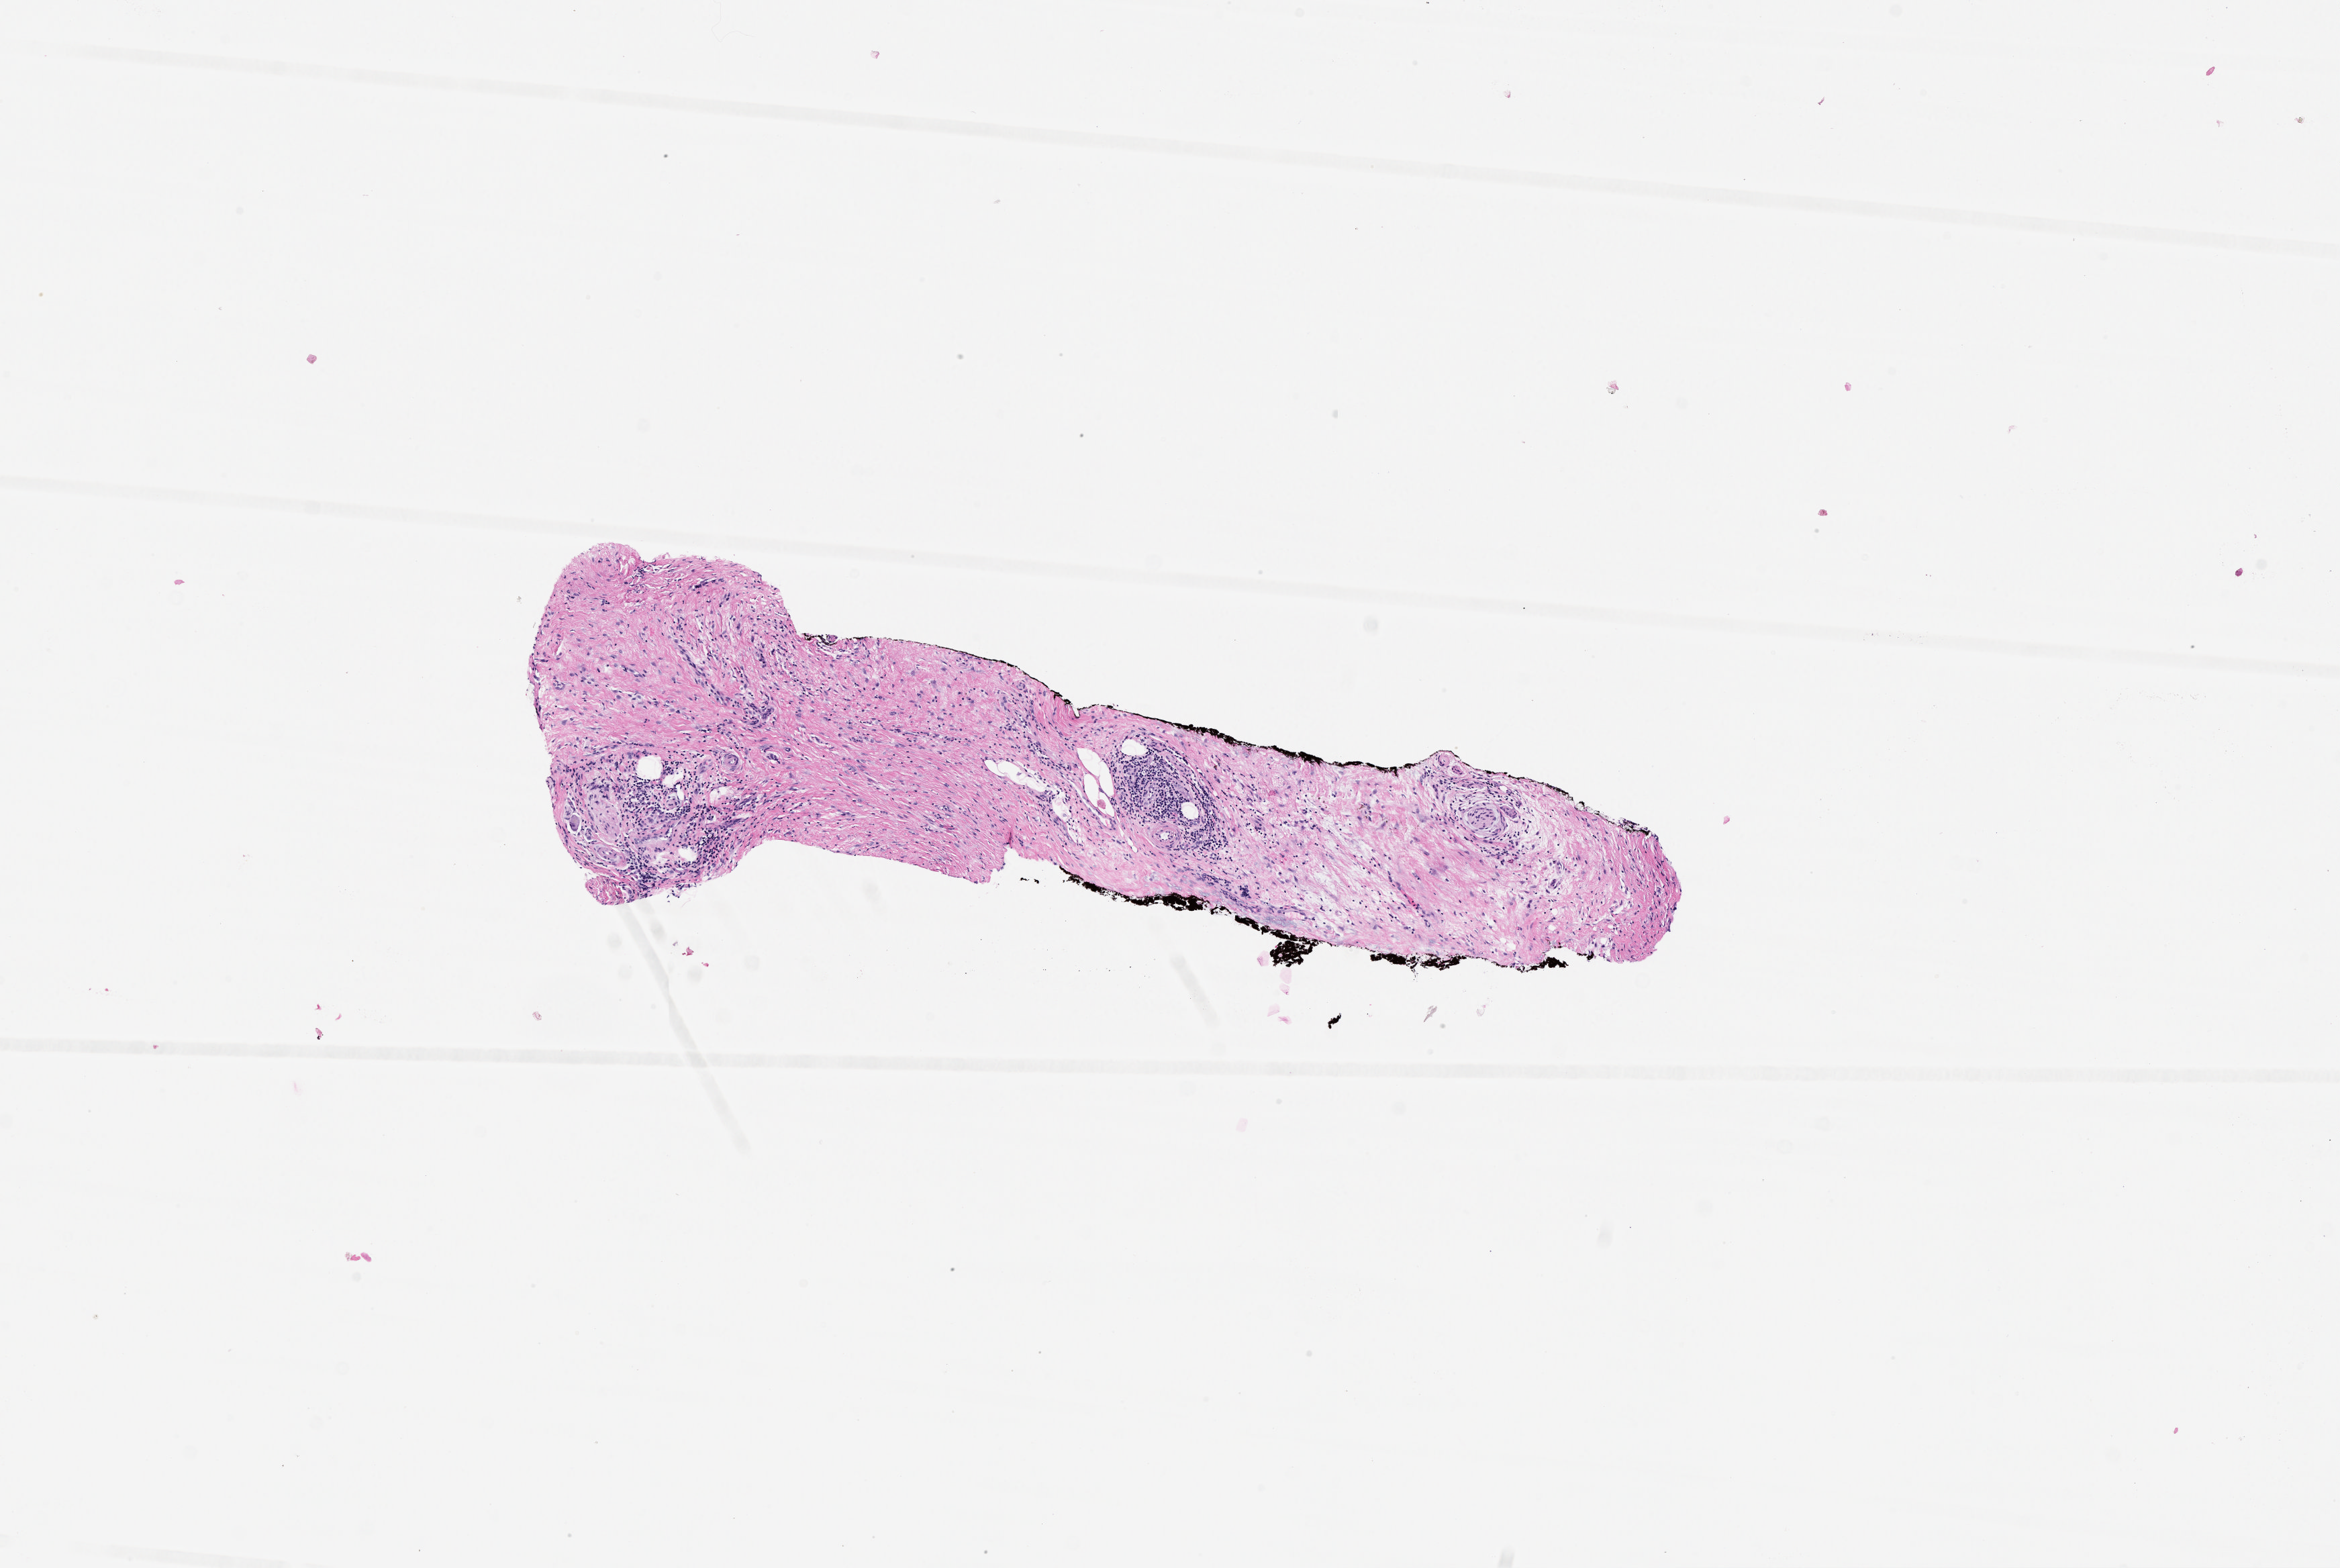
Hematoxylin and eosin (H&E) stained whole-slide image, a low-resolution overview of the entire scanned area, about 7.0 x 4.7 mm (from a 20x scan). Tumour tissue sample, pancreas. Female, 85 y/o. Histologic grade: G2 (moderately differentiated).
AJCC pathologic stage: IIA. Diagnosis: Infiltrating duct carcinoma, NOS. Primary tumour site (as recorded): head.